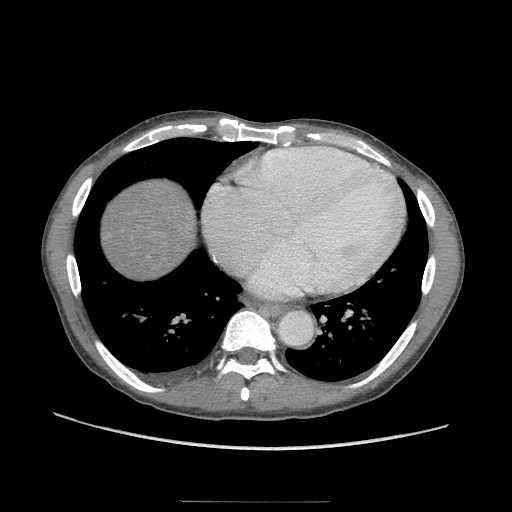
Contrast-enhanced abdominal CT (liver protocol), one axial slice. Slice 98 of 103 in the series (ordered by position). Soft-tissue window (W 400 / L 40 HU). 2.5 mm slice thickness. 512 × 512 image matrix, field of view 380 × 380 mm. From the clinical record (not read from this slice): diagnosis: hepatocellular carcinoma (patient treated with transarterial chemoembolisation; whether this scan precedes or follows treatment is not stated here); TNM stage (as recorded): Stage-IIIA; Child-Pugh class: A; tumour nodularity: multinodular.
Outlined on this slice (semi-automatic segmentation, software-assisted and operator-edited):
- abdominal aorta: bounding box [x1, y1, x2, y2] px = [278, 310, 311, 344]
- liver parenchyma outside the tumour (the mass and vessels are separate outlines, so this box may not span the whole liver): [106, 184, 188, 270]